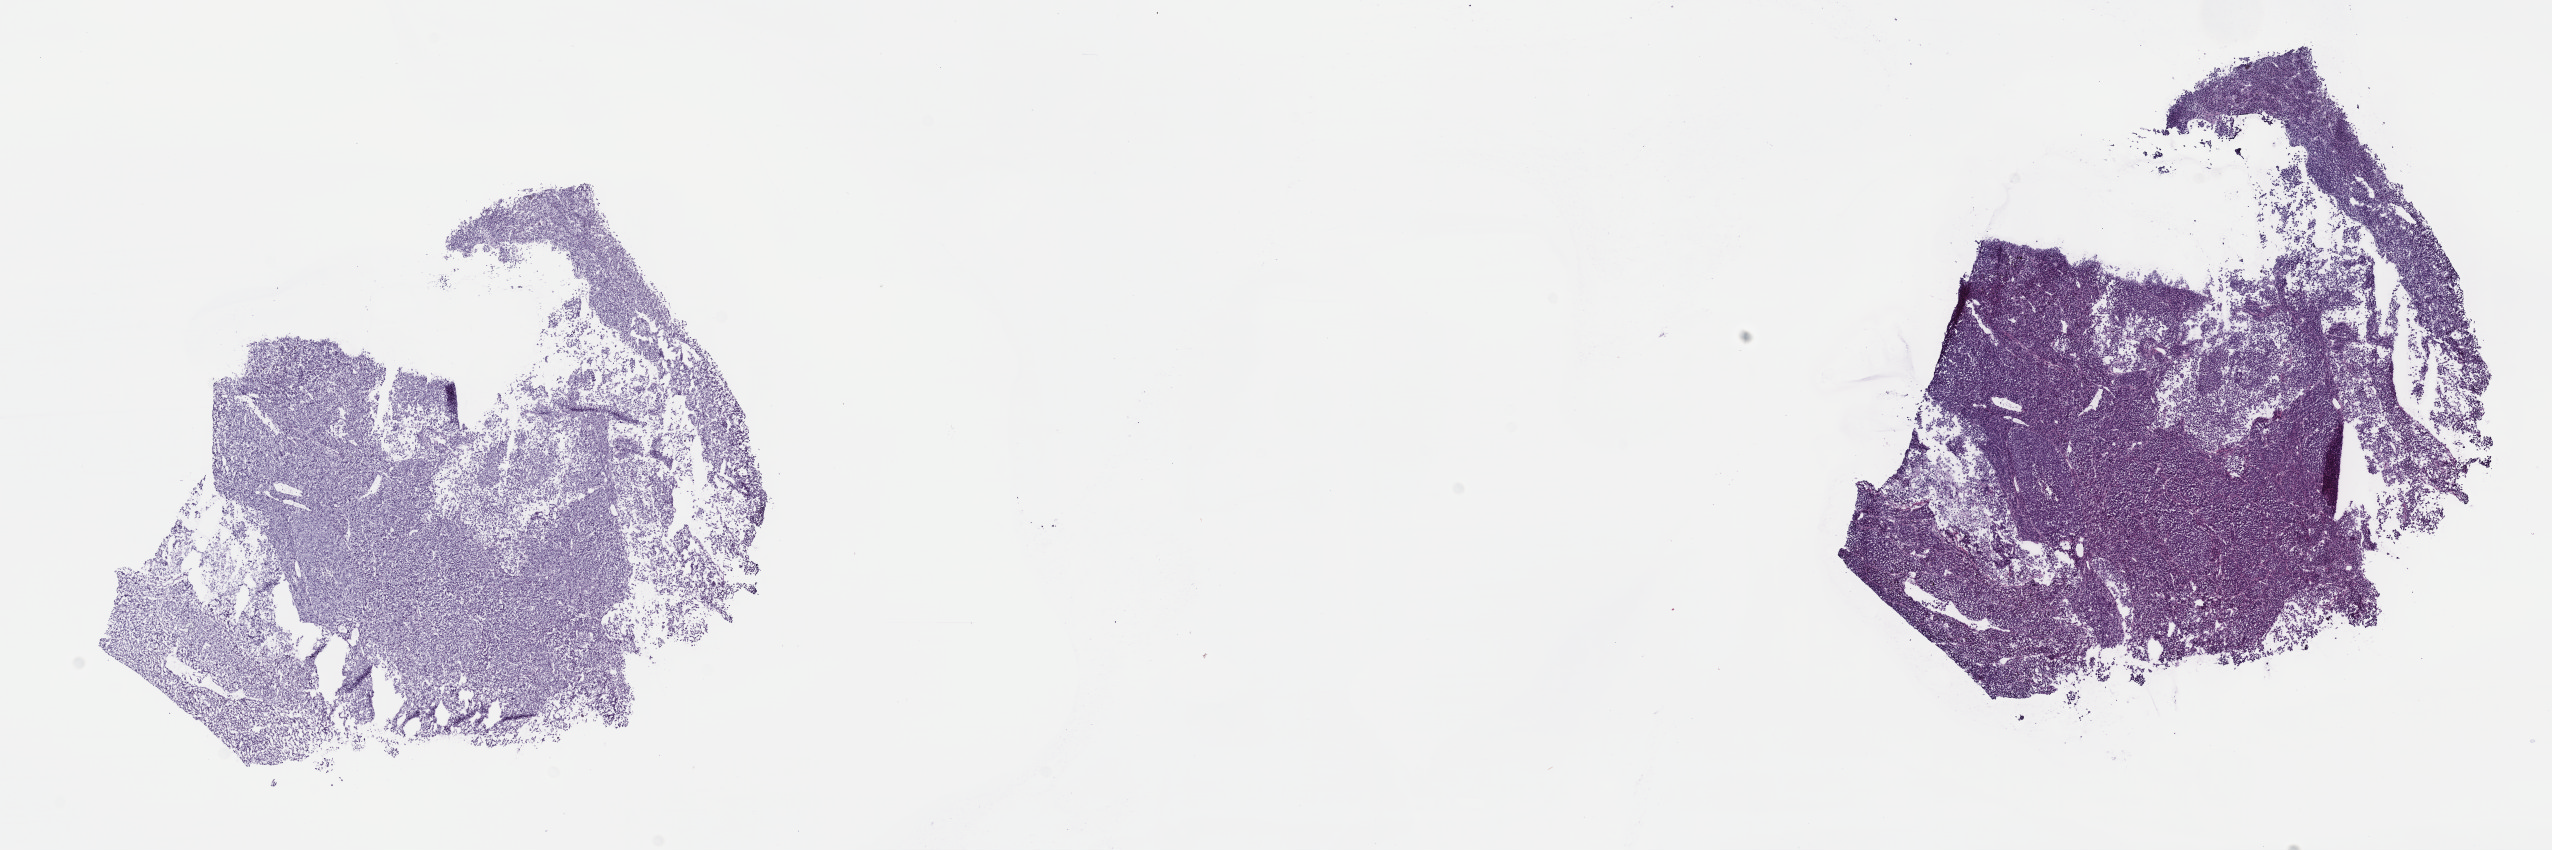
Whole-slide histology image, H&E-stained, shown as a low-resolution overview of the whole scanned area (about 20.6 x 6.9 mm, slide scanned at 40x); frozen section from the top of the tissue portion; sample: primary tumour, uvea. Female, age 49 years at initial diagnosis. Pathologist review of this section (percent, as recorded): tumour cells 97%, tumour nuclei 65%, normal cells 0%, stromal cells 0%, necrosis 3%. Infiltration values recorded for this section: lymphocyte infiltration 30%, monocyte infiltration 2%, neutrophil infiltration 0%.
Histologic diagnosis: Epithelioid cell melanoma (choroid). AJCC pathologic stage: IIIA (7th edition).